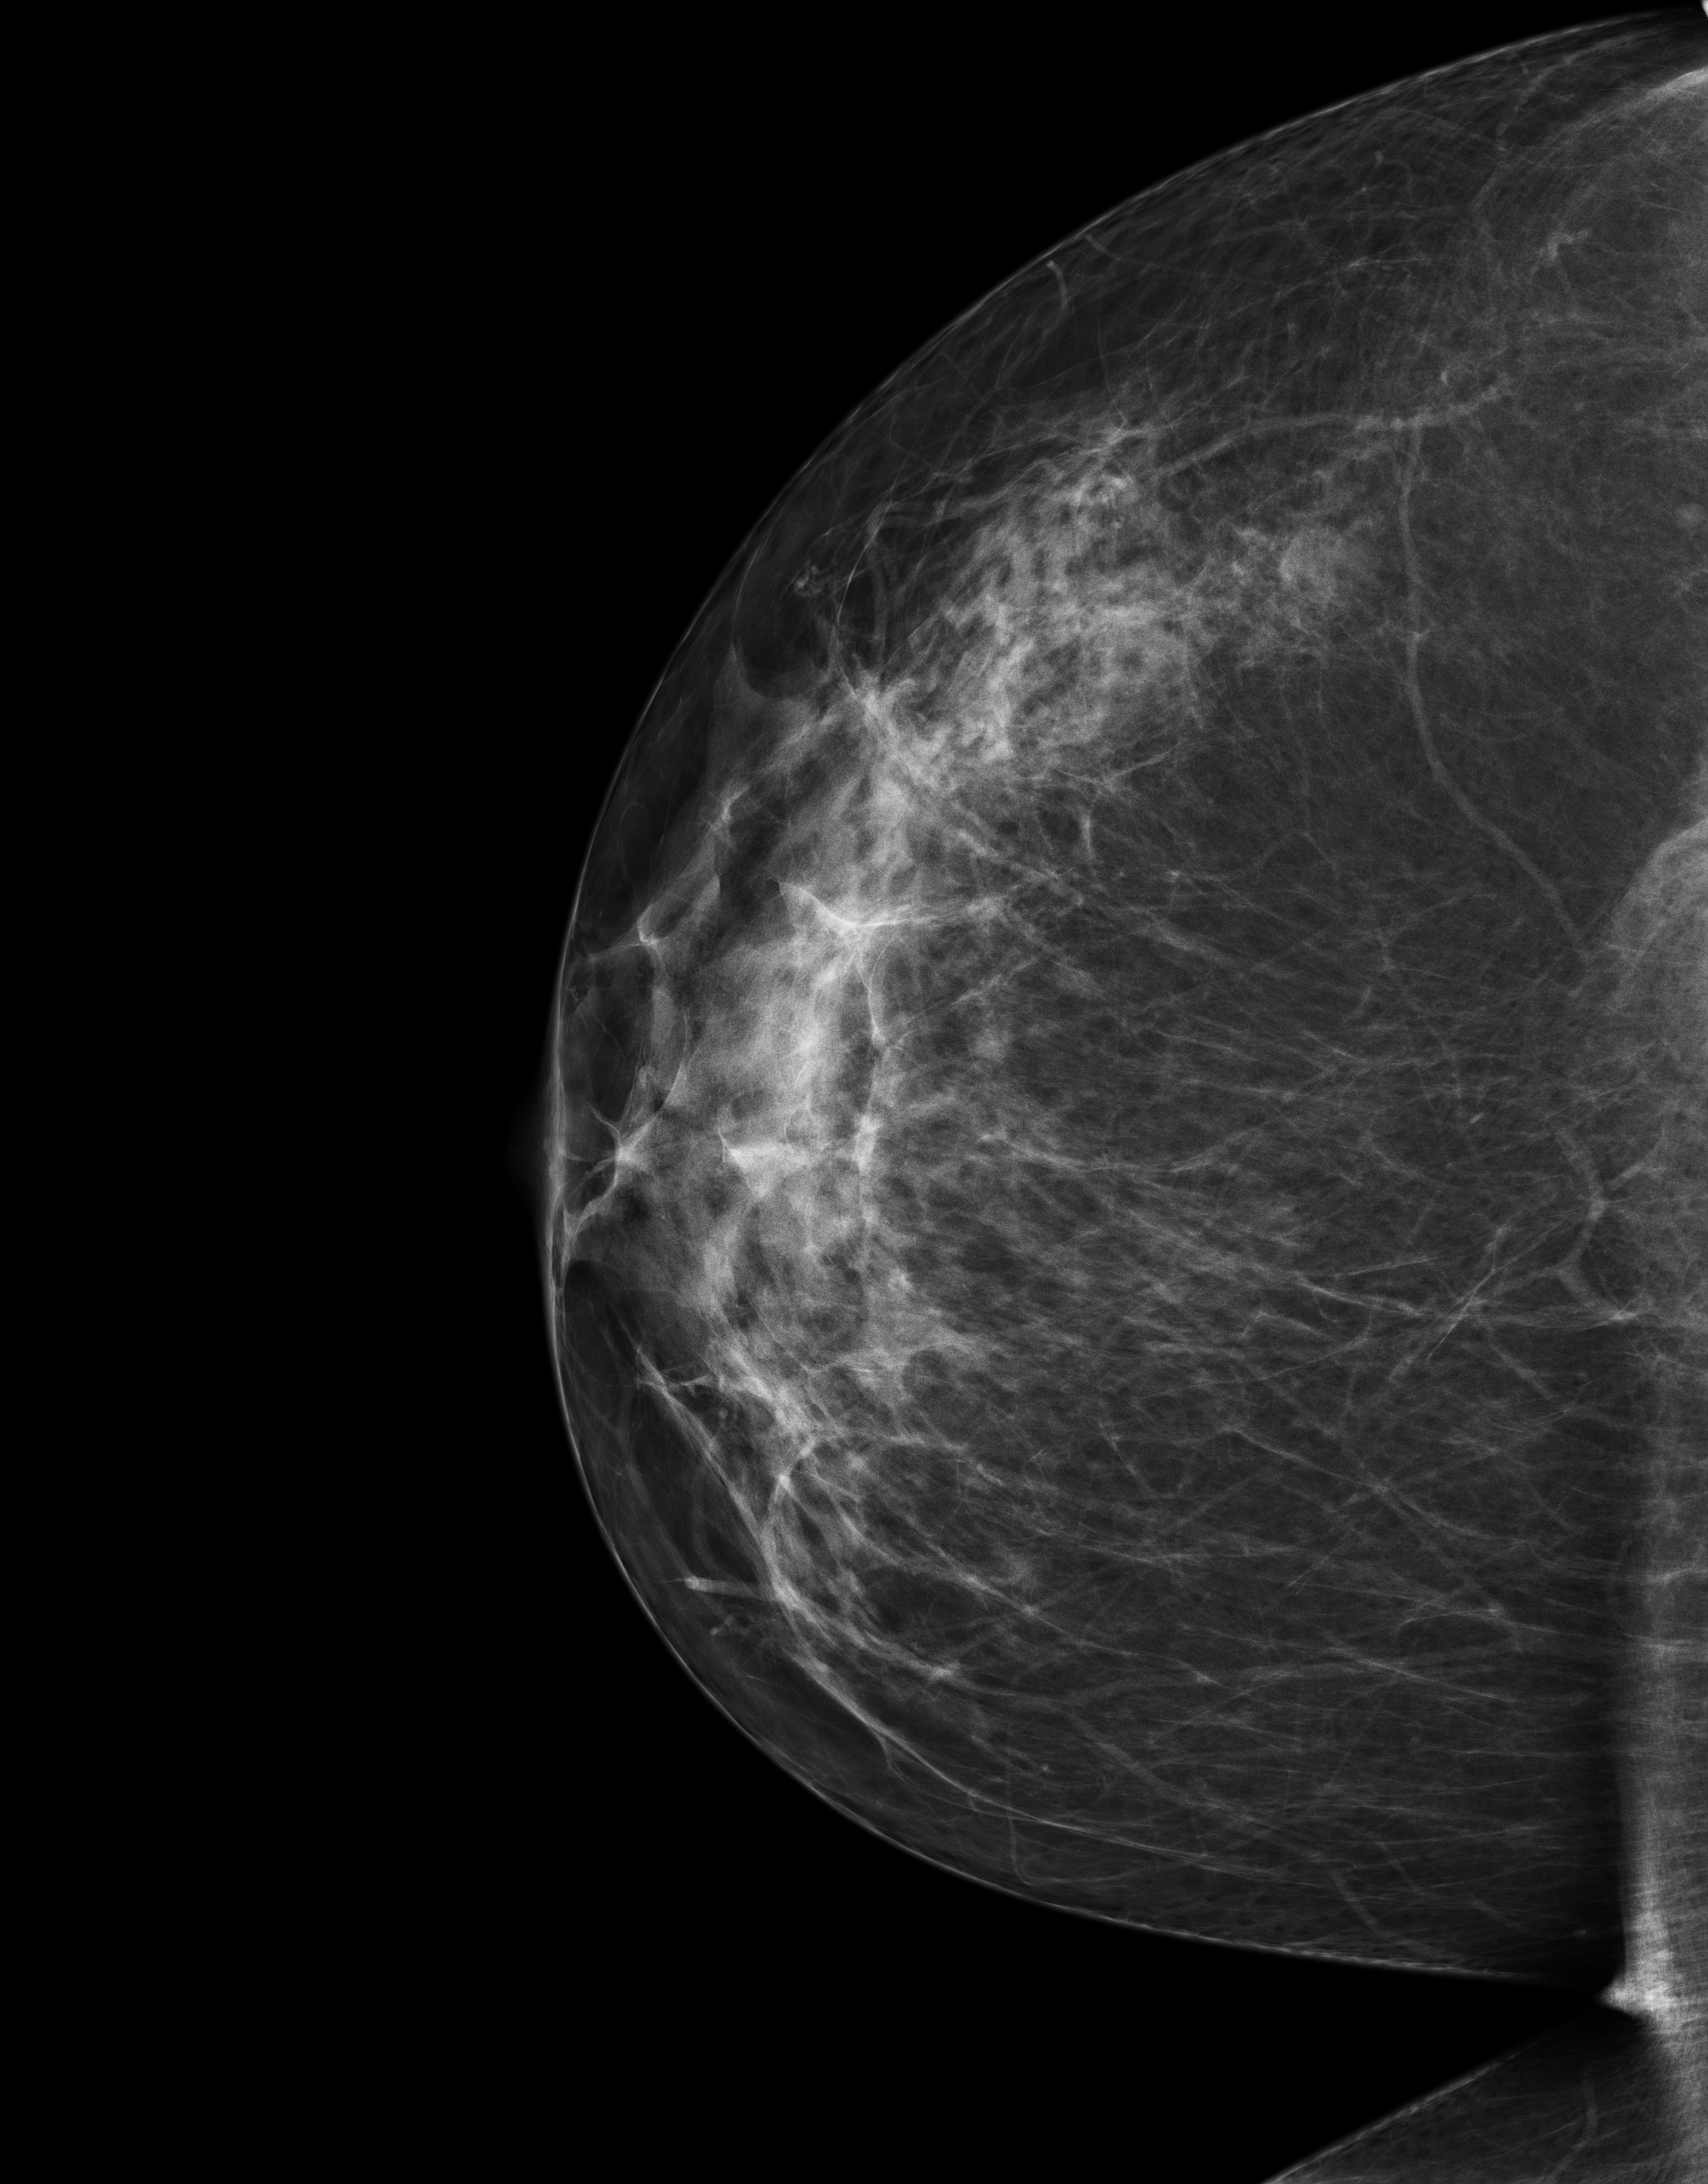
Full-field digital mammogram (FFDM); right breast; CC view; screening examination. Female patient, age 56 years.
BI-RADS breast density category at the screening exam (both breasts, scale 1–4): 3. Final BI-RADS assessment for this screening round (tomosynthesis exam, both breasts): category 1. Recall: no recall after this screen.